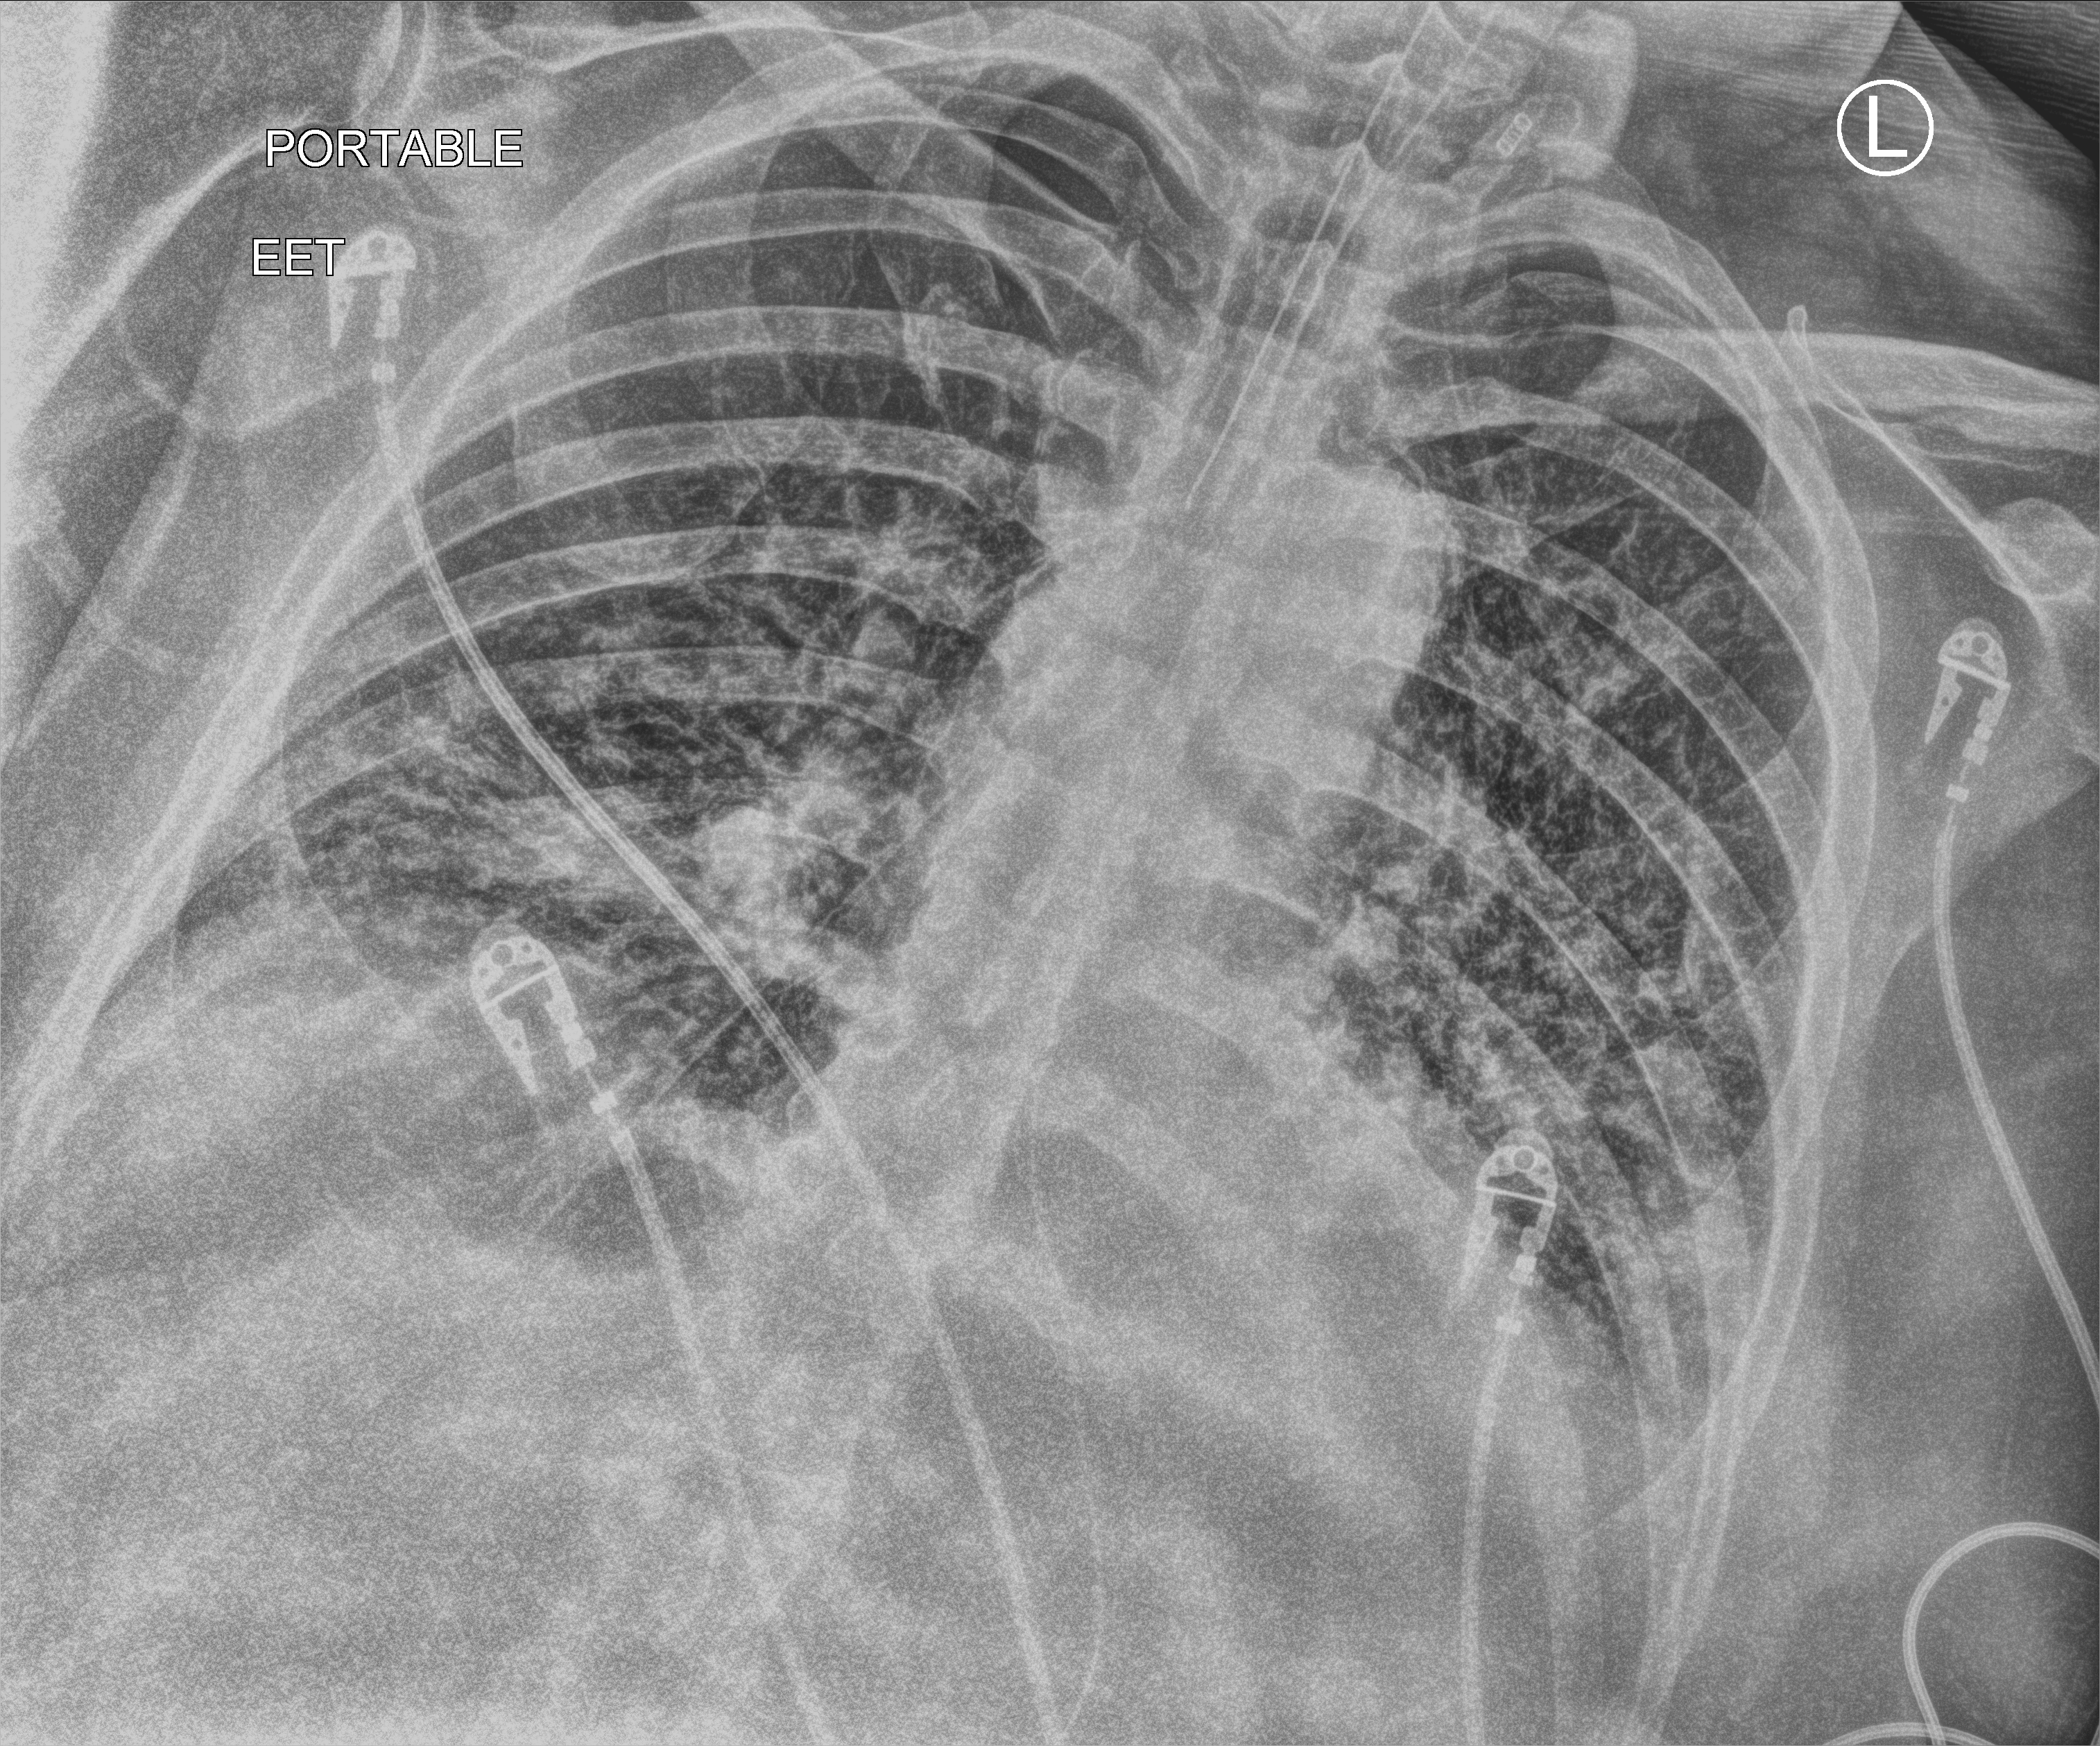
Chest X-ray (portable), anteroposterior (AP) projection. Patient hospitalised with COVID-19, aged 18–59 years.
Admission-level facts for this patient (not findings on this image; timing relative to this image not recorded):
- length of hospital stay: 9 days